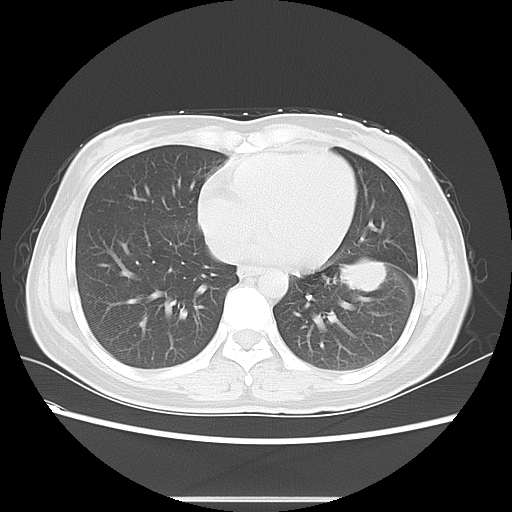
Chest CT, one axial slice; slice 23 of 55 in the series (ordered by position); reconstruction kernel LUNG; lung window (W 1500 / L -600 HU); 5 mm slice thickness; 512 × 512 image matrix, field of view 350 × 350 mm. Patient: female, 41 years. From the clinical record (not read from this slice): clinical TNM (as recorded): T1c N3 M1b.
Outlined on this slice (rectangle marked by the reading radiologist):
- lung tumour (recorded histology: adenocarcinoma): bounding box <338,255,387,300> (left, top, right, bottom; pixels)